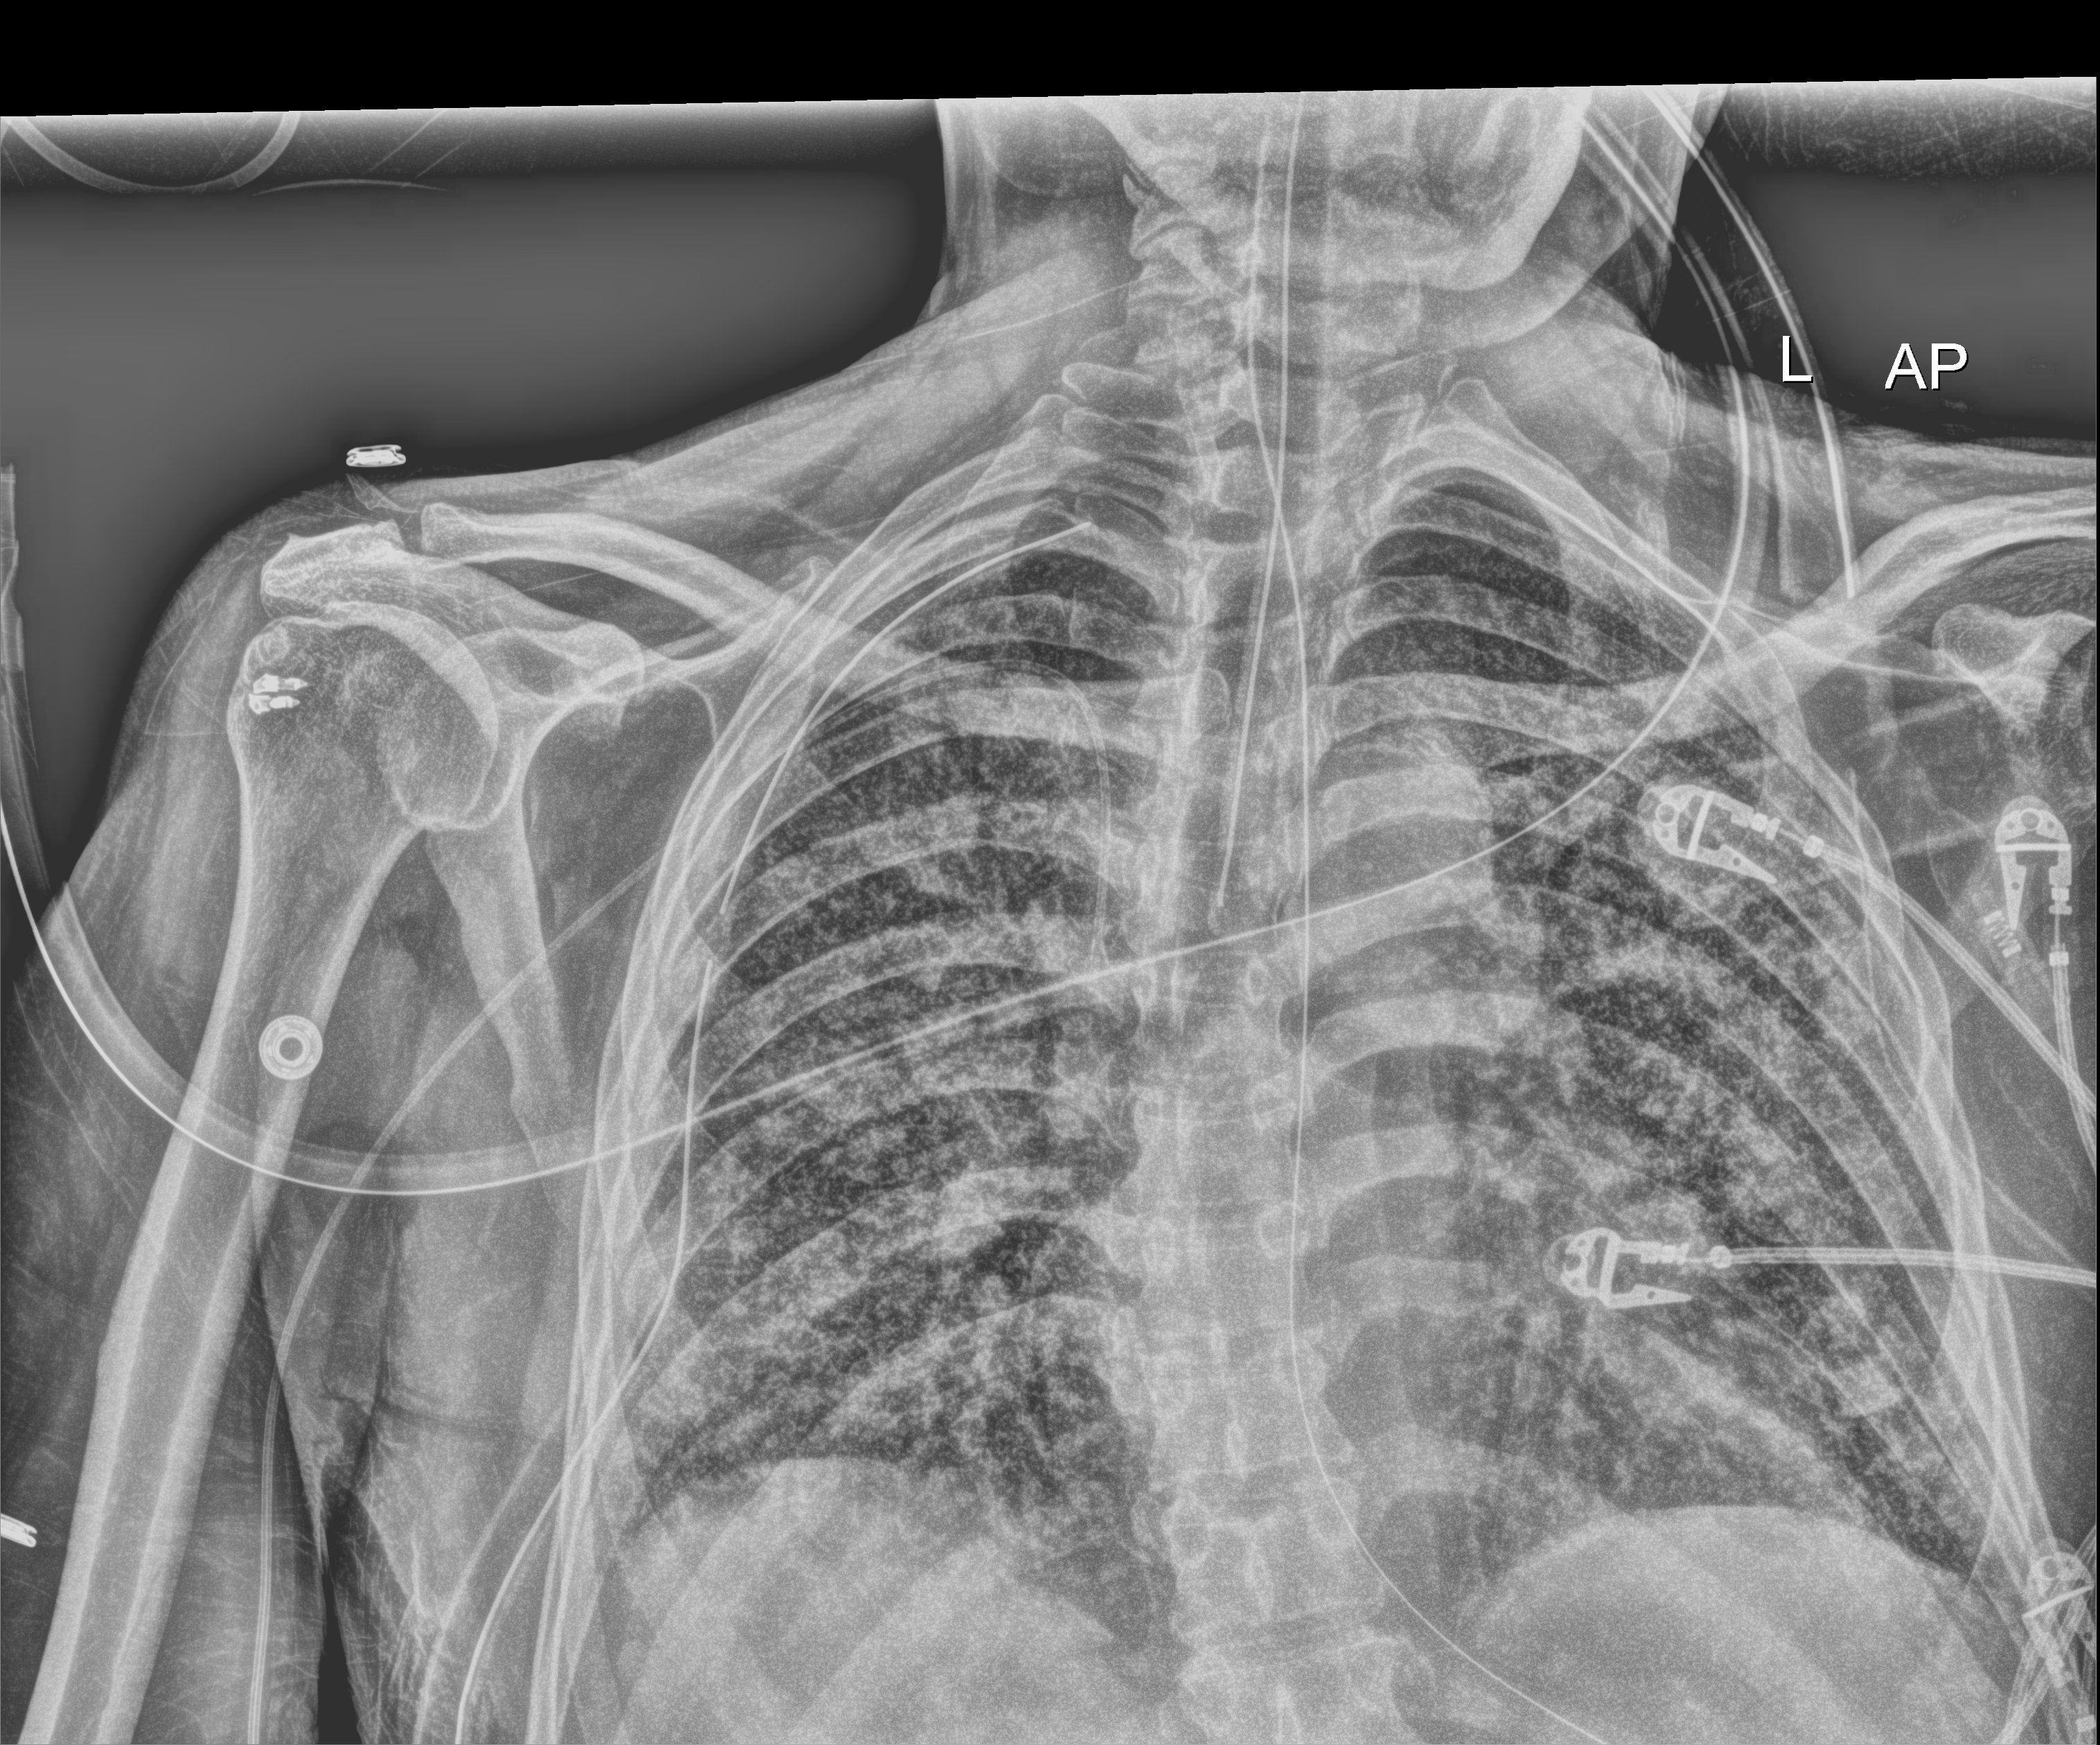
Chest X-ray (portable), anteroposterior (AP) projection. Patient hospitalised with COVID-19; male, aged 60–74 years.
From the hospital-stay record, not from the radiograph (when in the stay this image was taken is not recorded): admitted to intensive care during this hospital stay: yes; smoking status (admission record): never; length of hospital stay: 65 days.